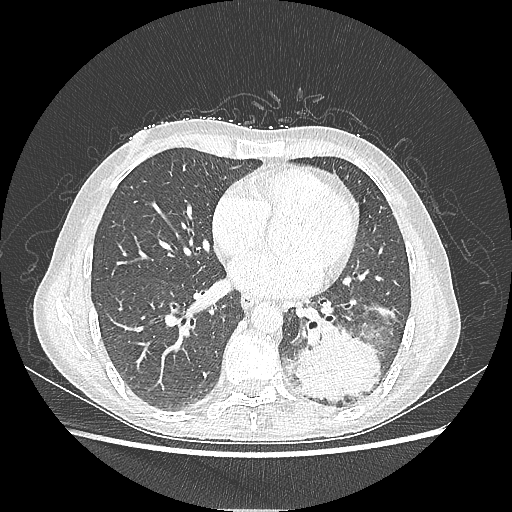
Chest CT, one axial slice; position 95 of 220 along the scan axis; reconstruction kernel LUNG; 80 kVp; lung window (W 1500 / L -600 HU); 1.25 mm slice thickness; 512 × 512 image matrix, field of view 360 × 360 mm. Female patient, age 53 years. From the clinical record (not read from this slice): clinical TNM (as recorded): T3 N0 M0.
Annotated regions visible in this slice (rectangle marked by the reading radiologist):
- lung tumour (recorded histology: adenocarcinoma): box from (x=287, y=320) to (x=383, y=403) px